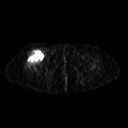
FDG PET of an extremity soft-tissue mass (from a PET/CT study), one axial slice; position 276 of 311 along the scan axis; 3.27 mm slice thickness; 128 × 128 image matrix, field of view 500 × 500 mm. Female patient, age 57 years. From the clinical record (not read from this slice): histological type: pleiomorphic undifferentiated sarcoma; grade: high; site of the primary tumour: right quadricep.
Outlined on this slice (expert contour drawn on MRI and transferred to this co-registered scan by the dataset authors):
- tumour plus oedema (research contour): bounding box (x1, y1, x2, y2) in pixels: (24, 49, 44, 68)
- tumour (research contour): (24, 49, 44, 68)